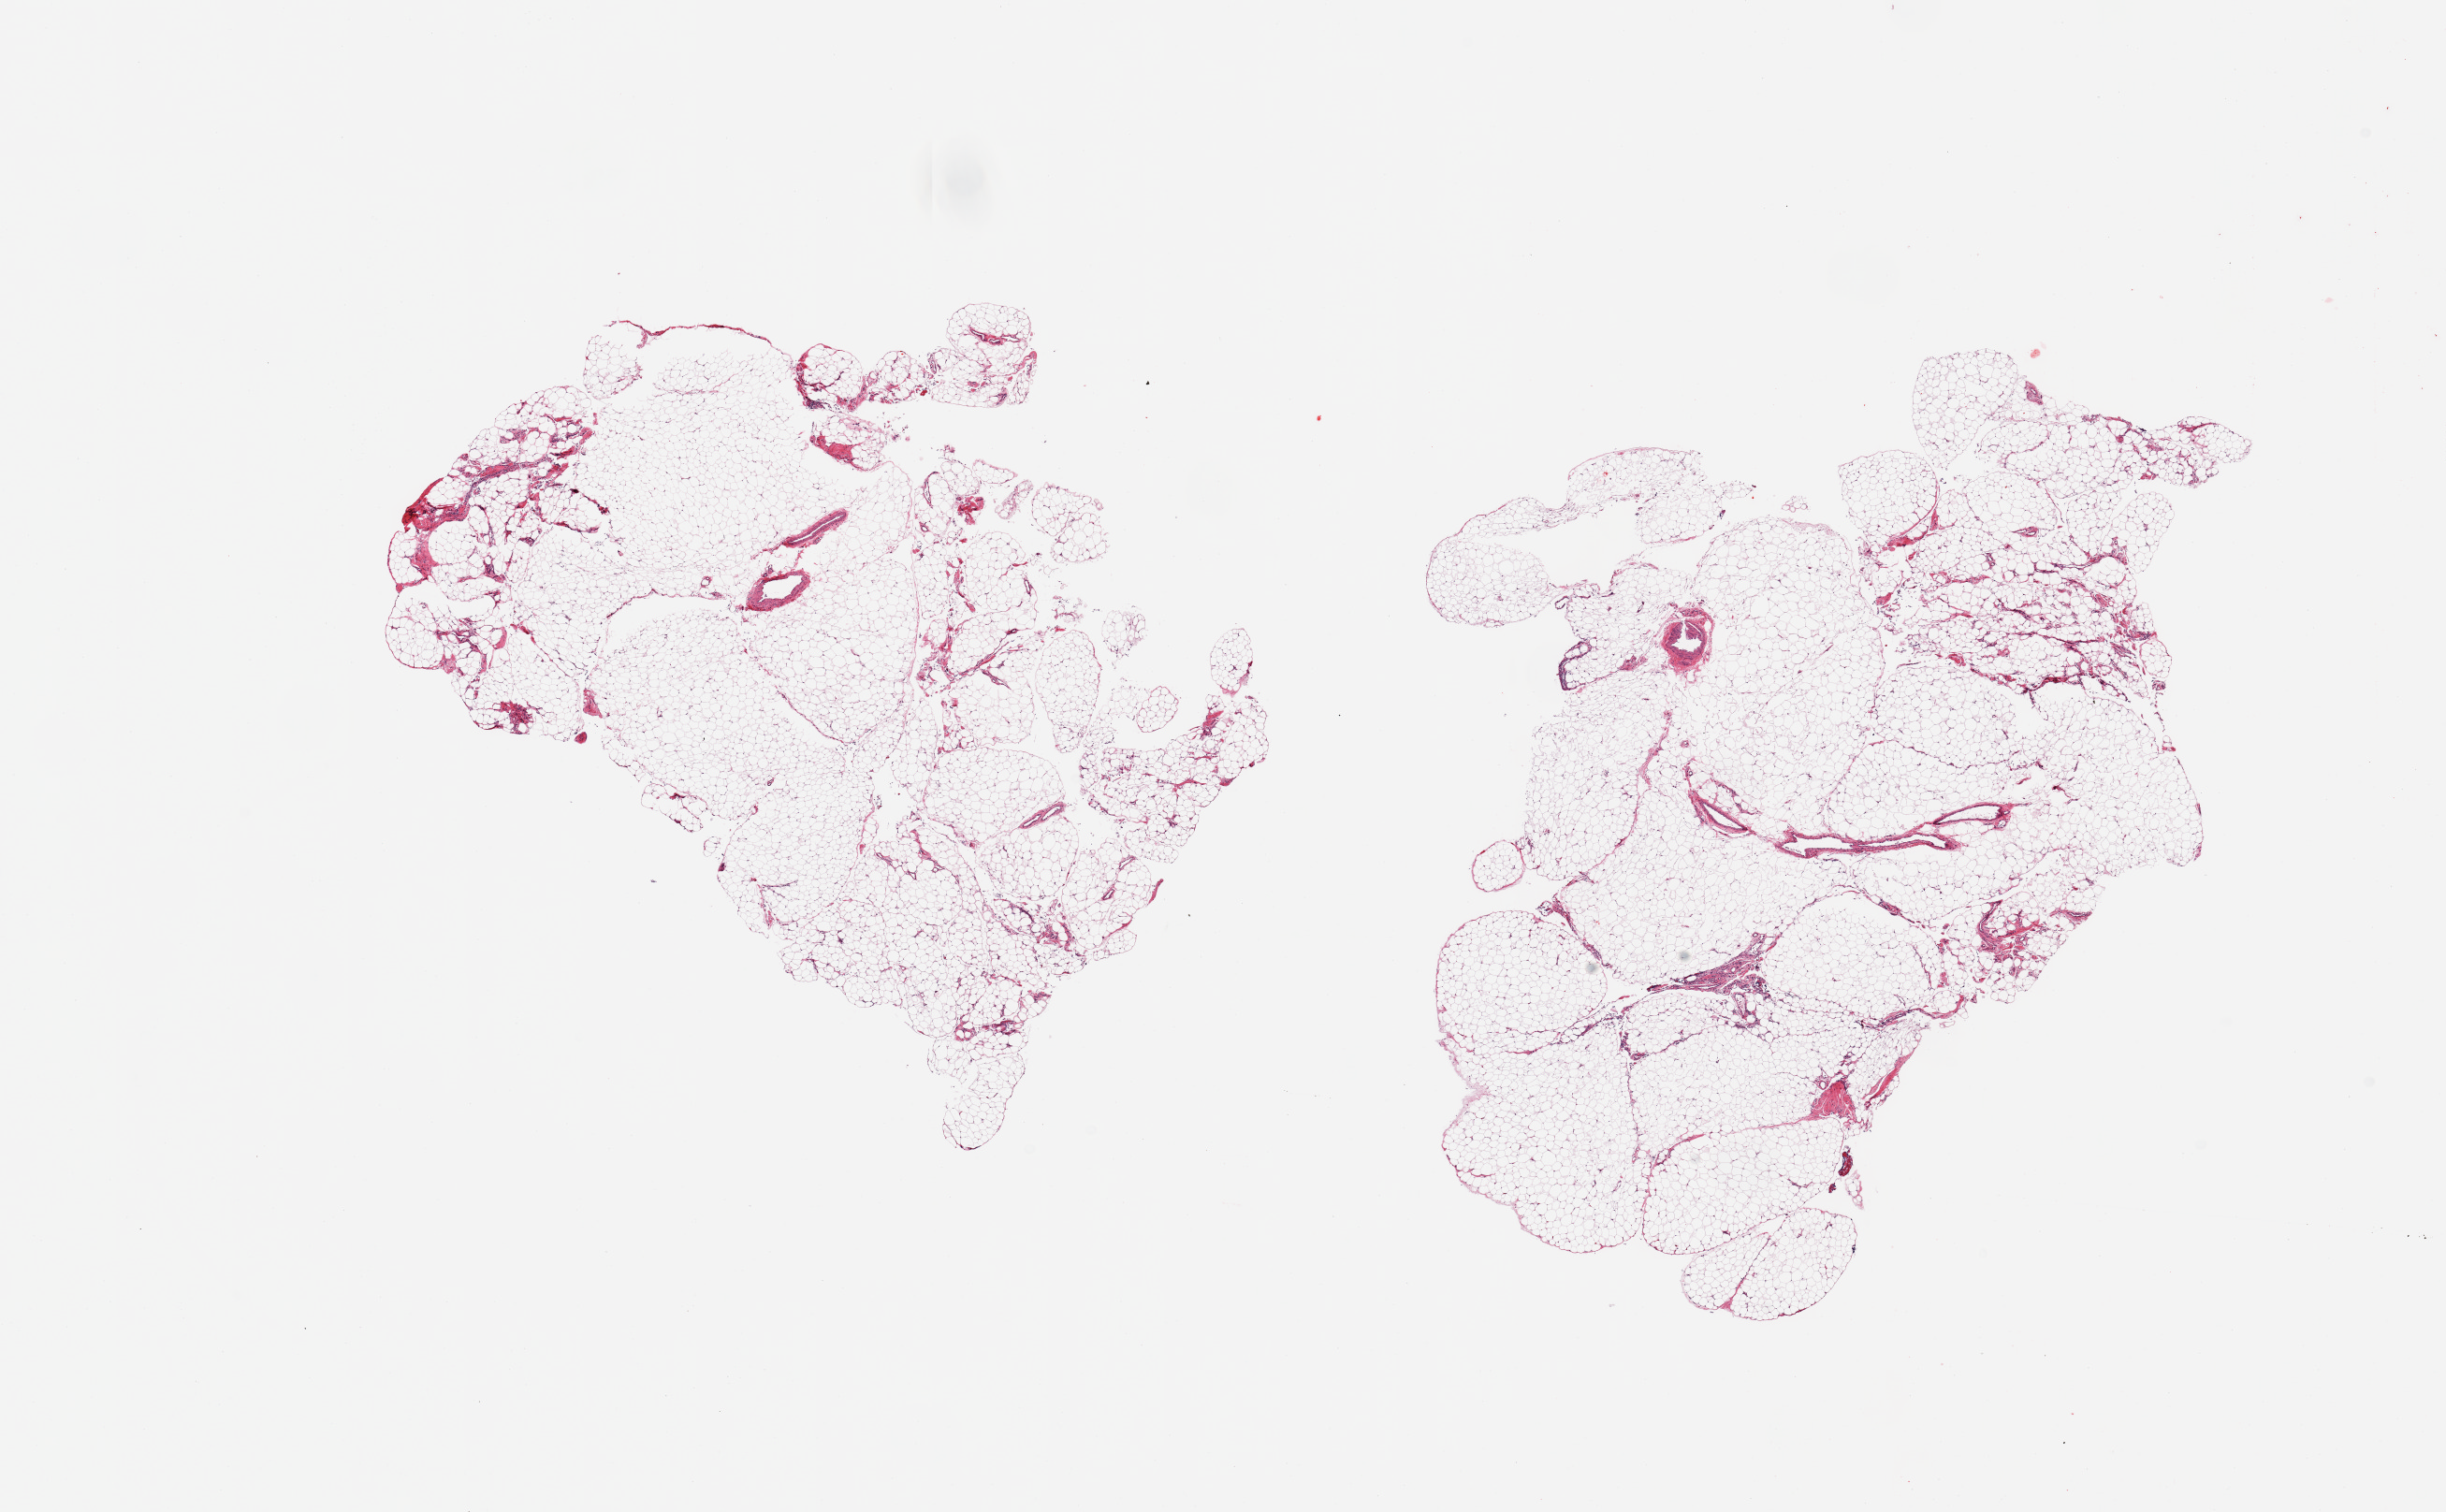
Whole-slide image, hematoxylin and eosin (H&E) stain — low-resolution overview of the scanned area, about 20.7 x 12.8 mm; PAXgene-fixed, paraffin-embedded tissue; target tissue: omentum; tissue donor sample. Donor sex: female.
Reviewer comment on this tissue sample: 2 pieces; minimal fibrovascular component.